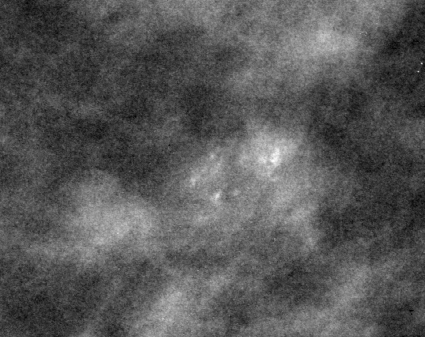
Cropped region of a digitized screen-film mammogram centred on a radiologist-marked abnormality; left breast; CC view.
Marked abnormality: calcifications, morphology pleomorphic, distribution clustered; BI-RADS assessment category 4; pathology (as recorded): benign.